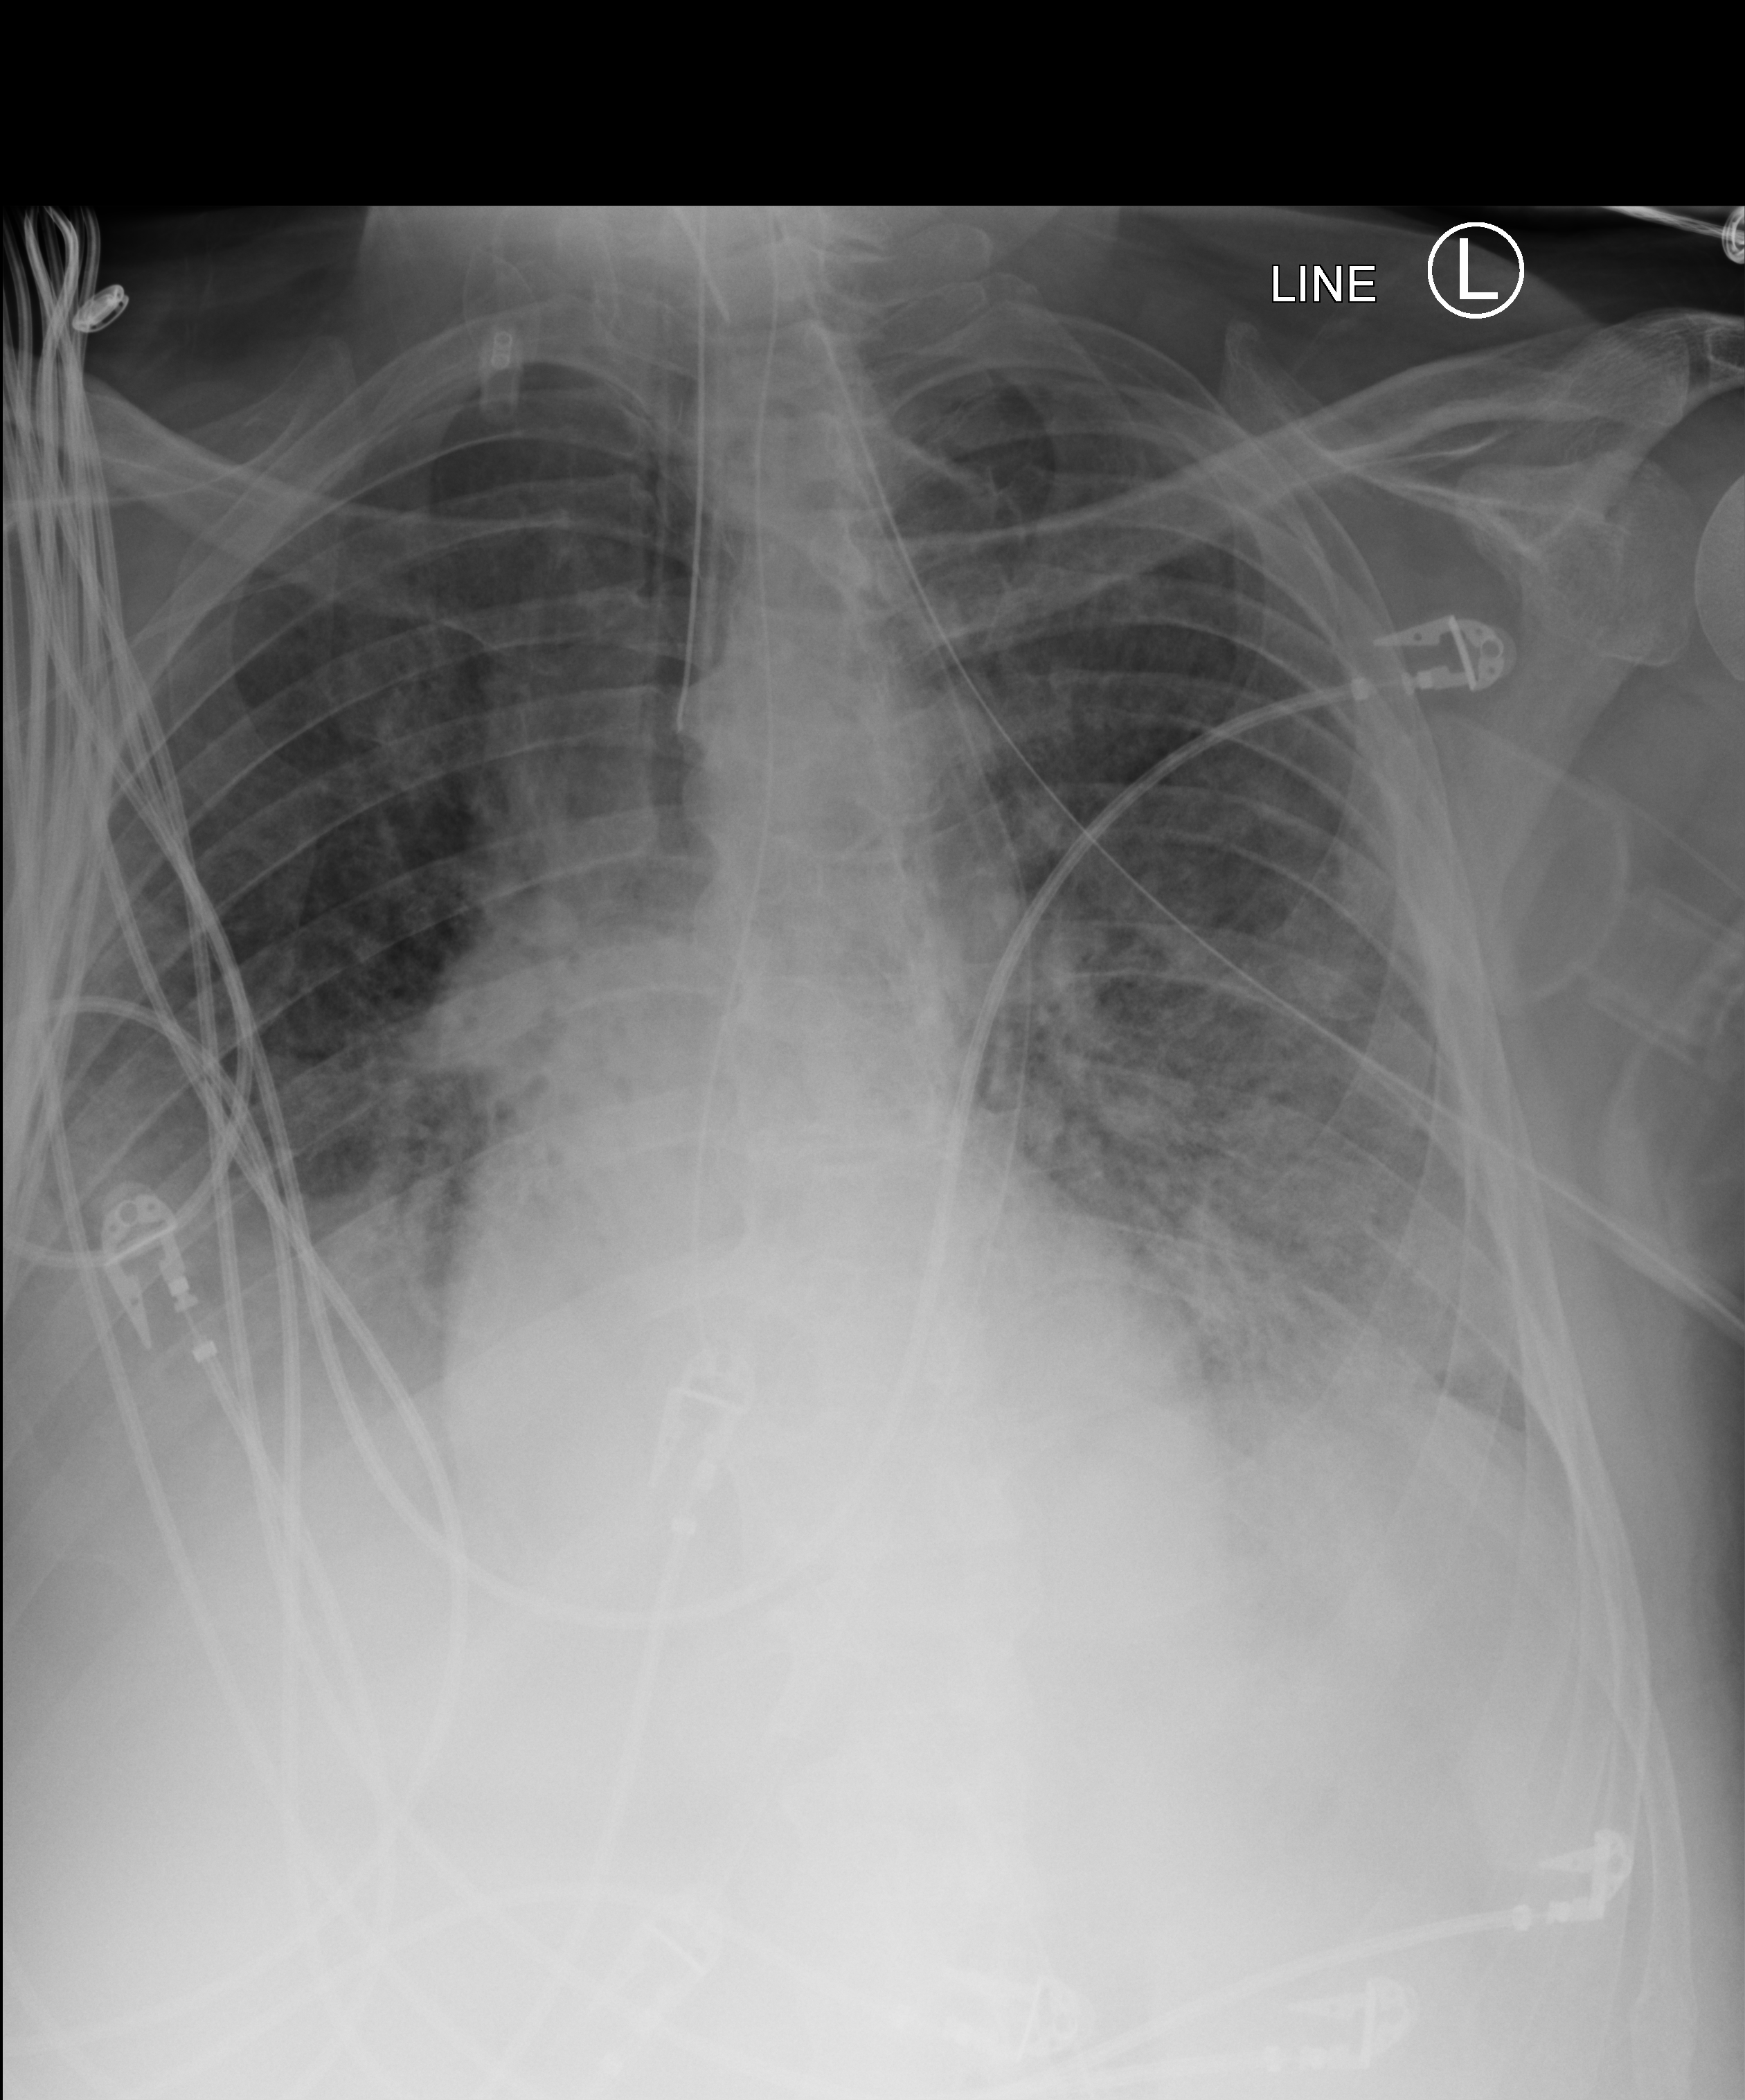
Chest X-ray (portable), anteroposterior (AP) projection. Patient hospitalised with COVID-19; male, aged 60–74 years.
Hospital-stay facts (about this admission, not read from this image; timing relative to this image not recorded): chronic kidney disease (admission record): no; length of hospital stay: 15 days.